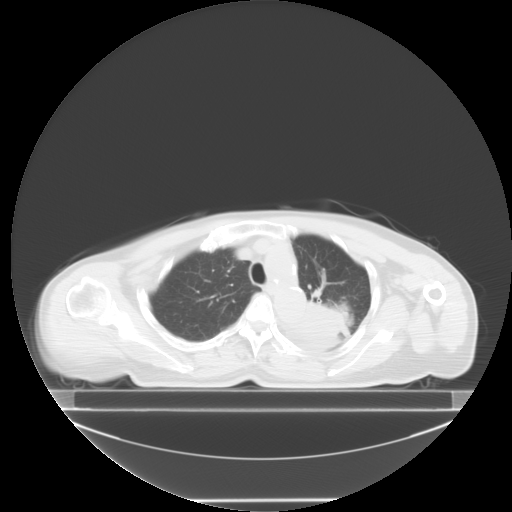
Chest CT, one axial slice. 120 kVp. Lung window (W 1500 / L -600 HU). 512 × 512 image matrix. Patient: female, 74 years. Case-level facts recorded for this patient, not image findings: clinical TNM (as recorded): T3 N1 M1c; histopathological grade: G3.
Annotated regions visible in this slice (bounding box drawn by a radiologist):
- lung tumour (recorded histology: small cell carcinoma): bounding box <295,300,351,362> (left, top, right, bottom; pixels)